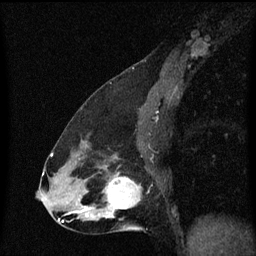
Breast MRI (dynamic contrast-enhanced), one sagittal slice; position 33 of 60 along the scan axis; dynamic contrast-enhanced series, image 2 of 3 at this slice position (ordered by acquisition); 1.5 T; TE 4.2 ms, TR 8.4 ms; 256 × 256 image matrix, field of view 200 × 200 mm. Patient: female, 47 years.
Outlined on this slice (semi-automatically segmented with operator editing):
- analysis volume of interest (the breast-tissue region the enhancement analysis was run in; not a lesion): bounding box [x1, y1, x2, y2] px = [100, 172, 142, 219]
- tumour enhancement mask (voxels above the 70 % enhancement threshold inside the analysis volume of interest): [106, 174, 141, 211]